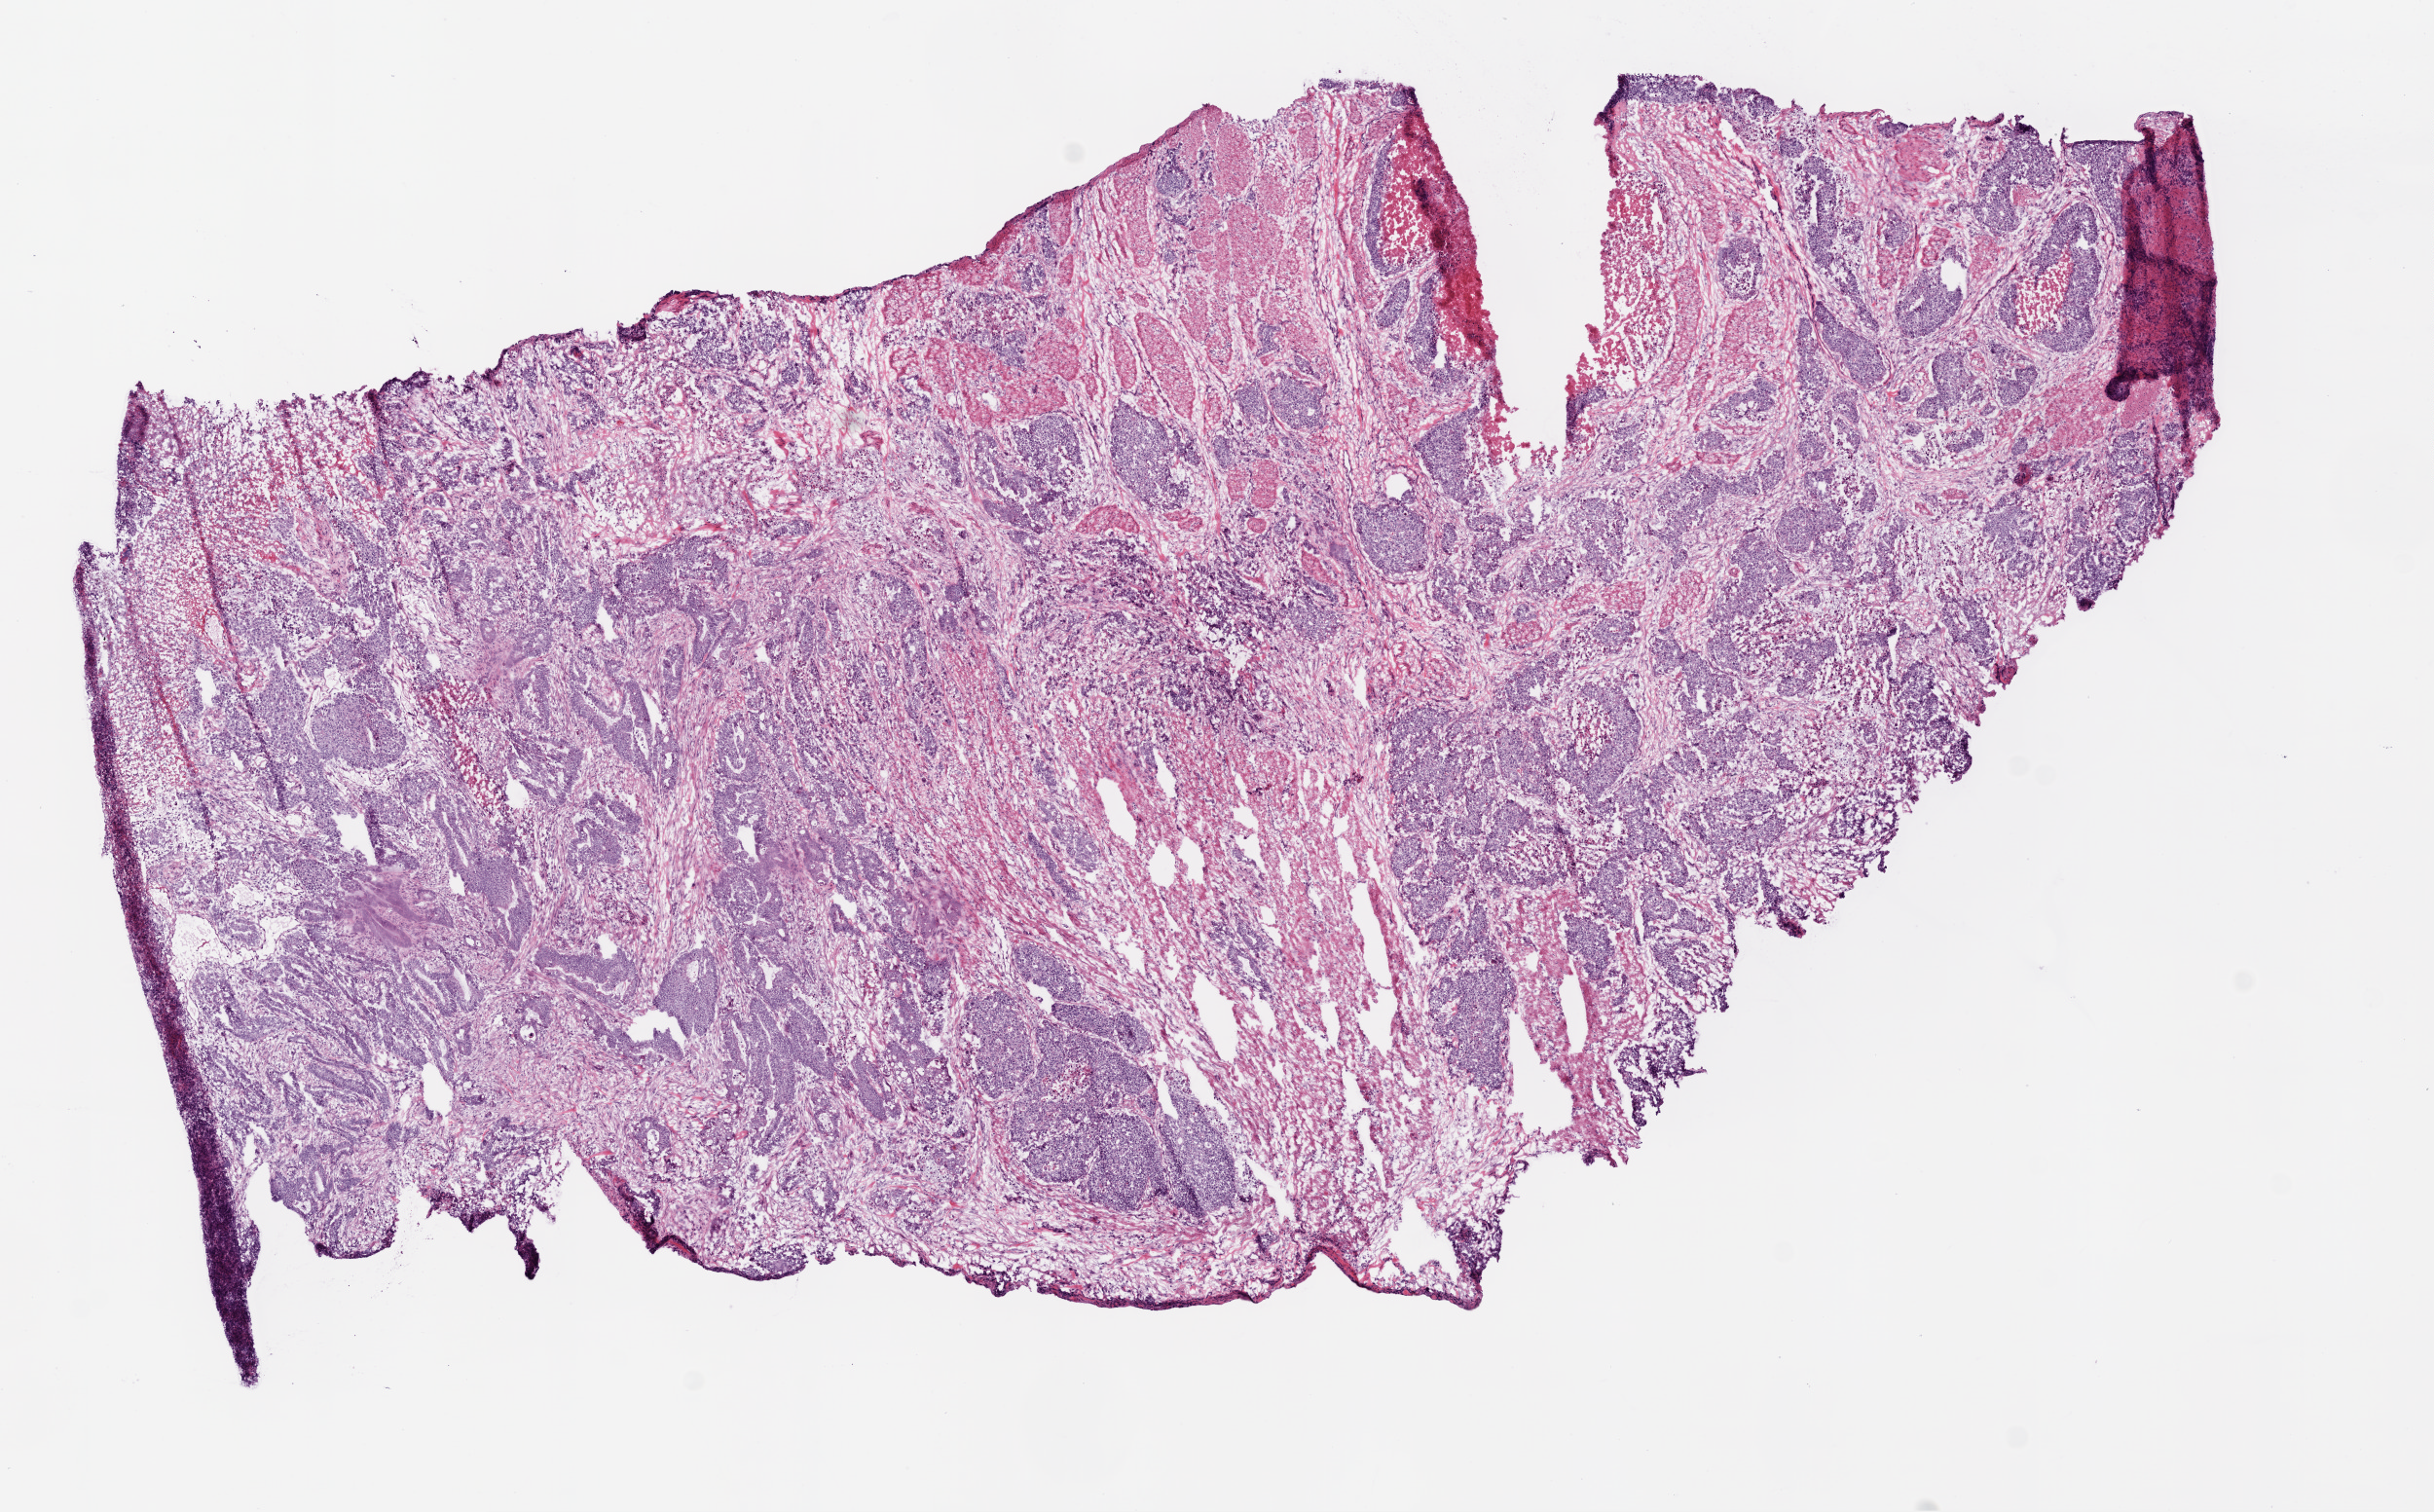
H&E-stained whole-slide image — shown as a low-resolution overview of the whole scanned area (about 10.0 x 6.2 mm), frozen section, rectum, primary tumour sample. Female, age 84 years at initial diagnosis. Pathologist review of this section (percent, as recorded): tumour cells 70%, tumour nuclei 80%, normal cells 0%, stromal cells 25%, necrosis 5%.
AJCC pathologic stage: IV (5th edition). Lymph nodes positive (case pathology): 5 of 17 examined. Histologic diagnosis: Adenocarcinoma, NOS.